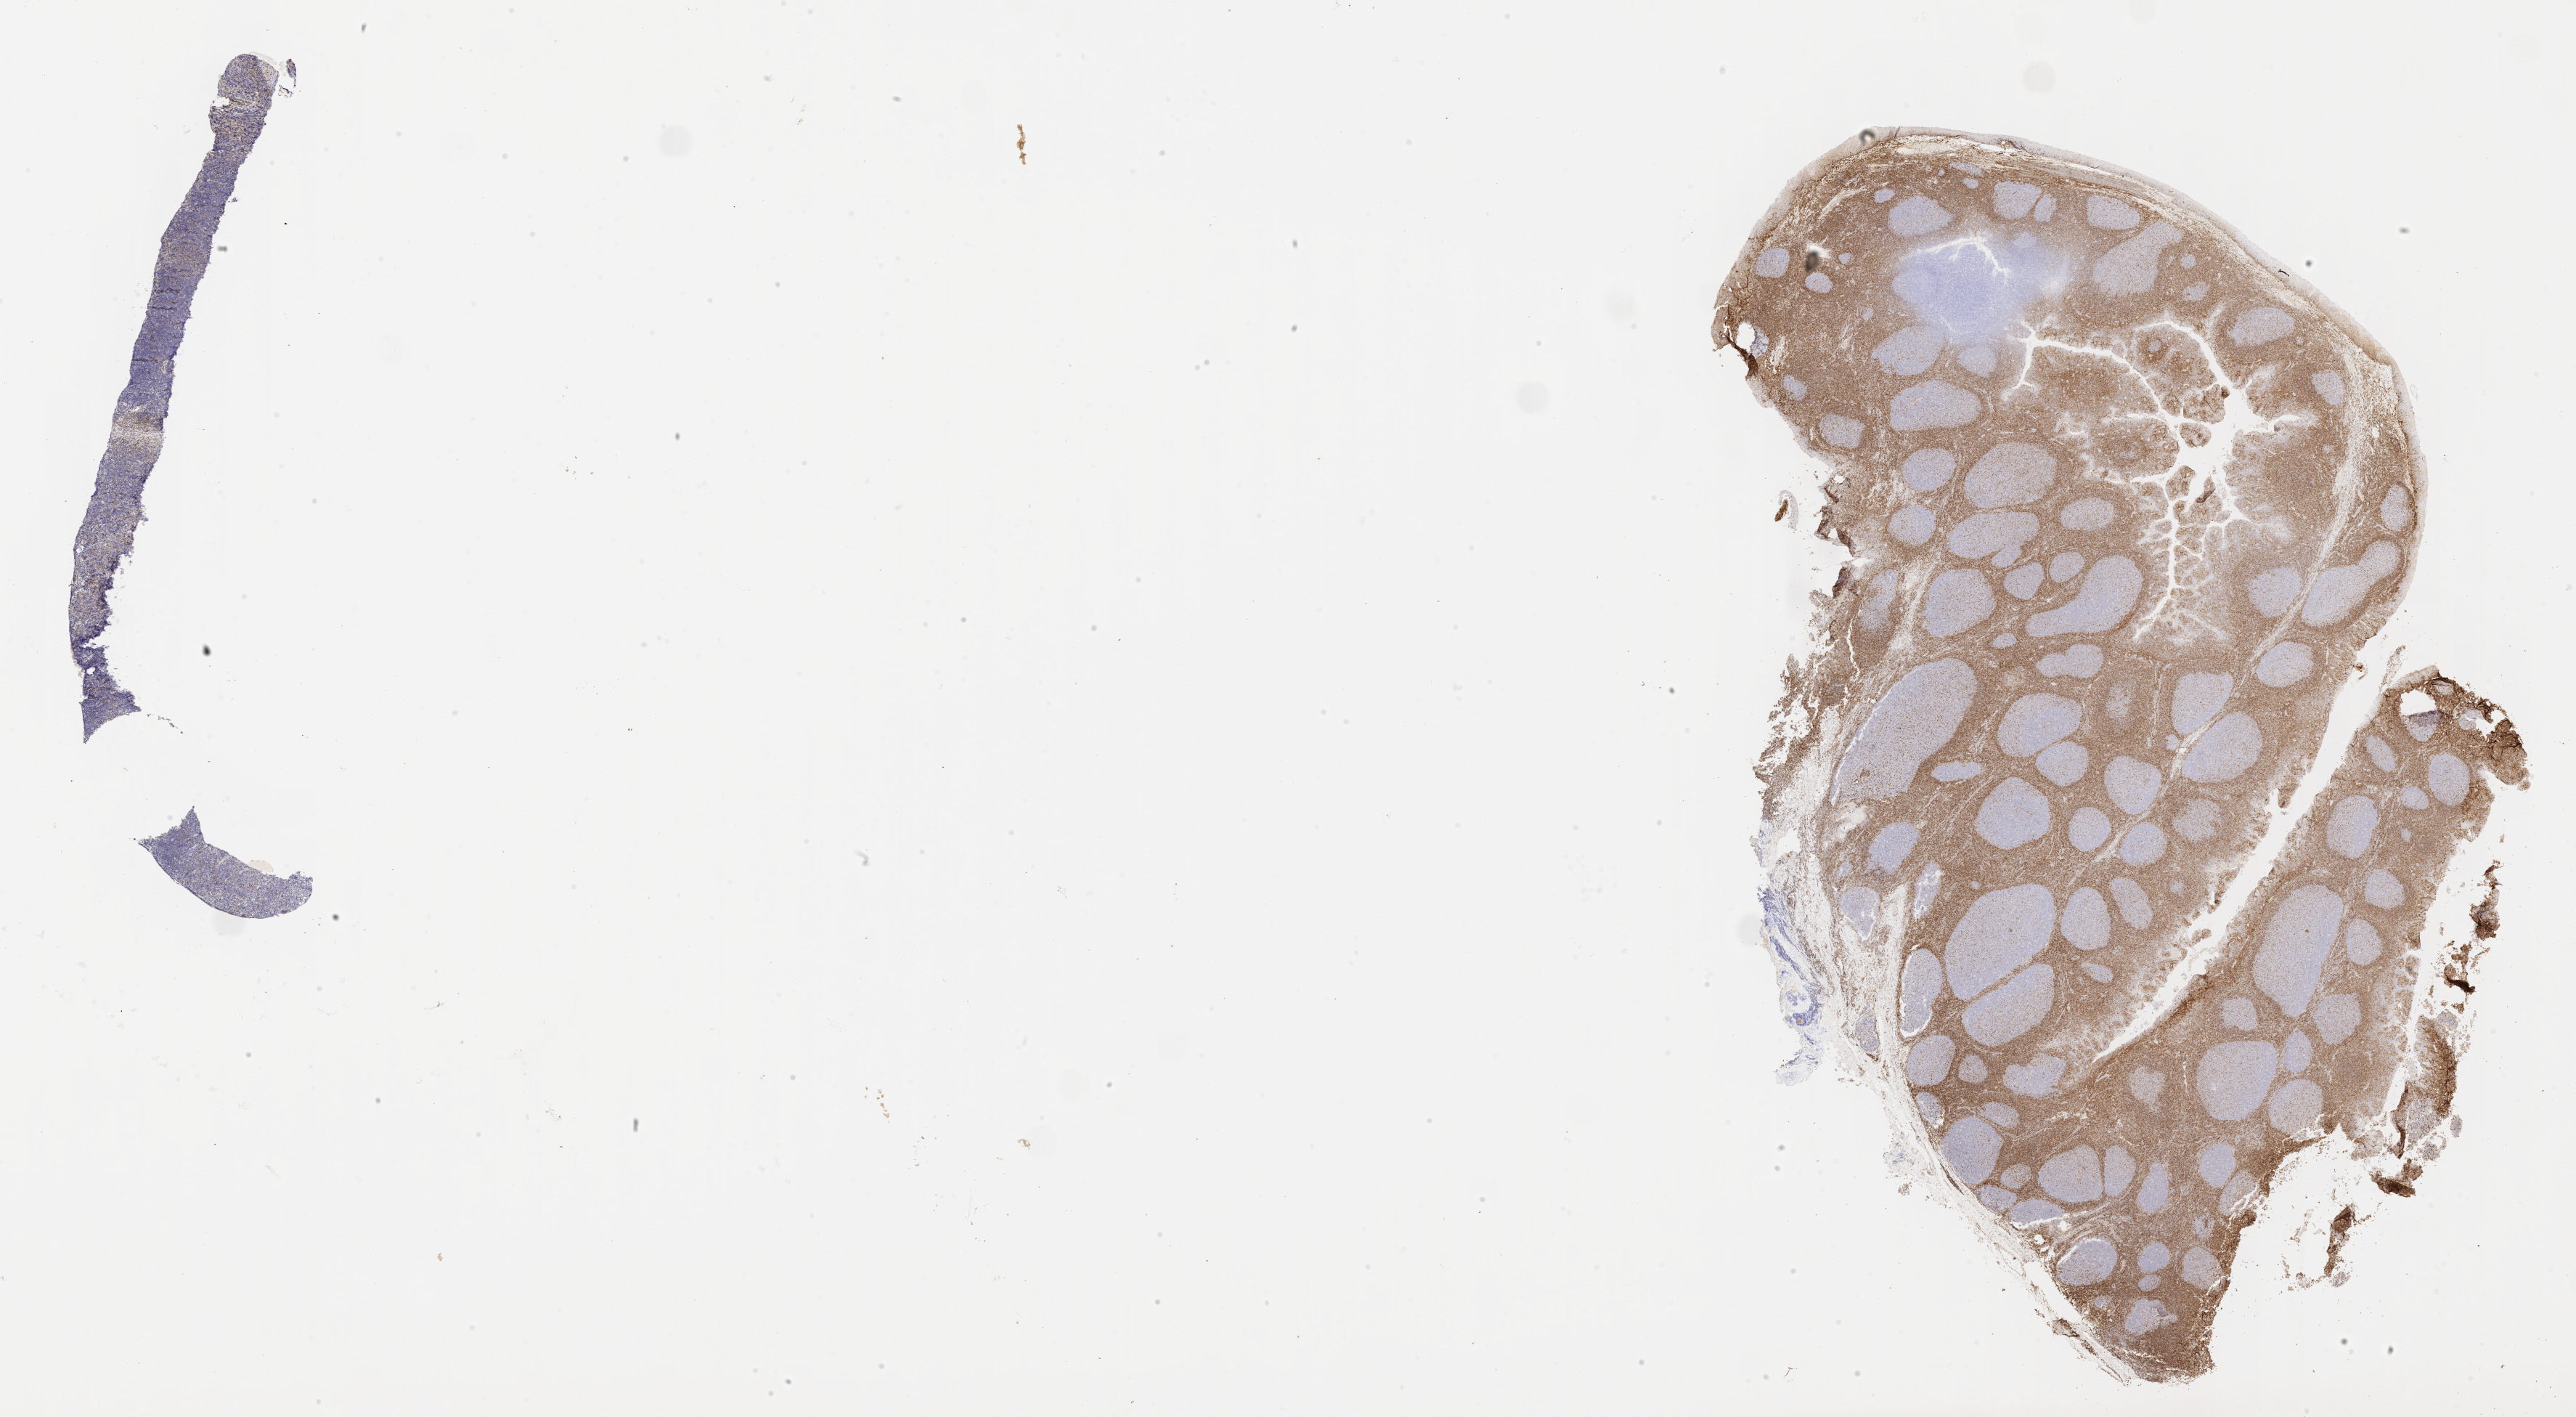
Whole-slide image, immunohistochemical stain for BCL2 — whole scanned area (about 28.7 x 15.8 mm) shown as a low-resolution overview. Specimen: tumor tissue. Site: ovary. Female patient; age at initial diagnosis 9 years.
• diagnosis: Burkitt lymphoma, NOS